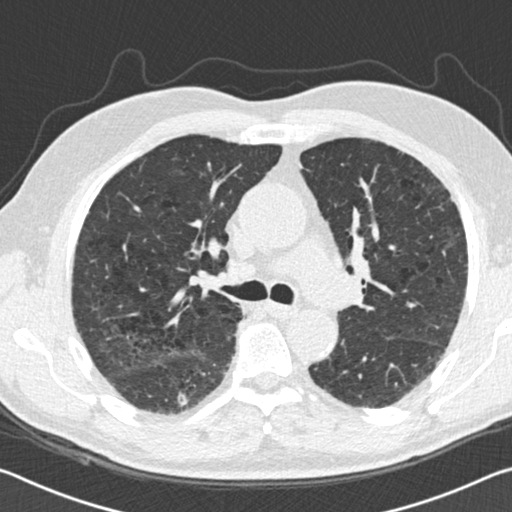
Low-dose screening chest CT, one axial slice. Slice 87 of 142 in the series (ordered by position). Reconstruction kernel B30f. 120 kVp. Lung window (W 1500 / L -600 HU). 2 mm slice thickness. 512 × 512 image matrix, field of view 340 × 340 mm.
Structures marked on this image (outlined manually by an expert reader):
- lesion 1 (tumor, lower lobe of right lung): bounding box <177,391,189,407> (left, top, right, bottom; pixels)